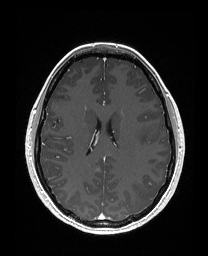
Brain MRI from a brain-tumour surgery series, one axial slice; slice 100 of 176 in the series (ordered by position); T1-weighted post-contrast; 1 mm slice thickness; 208 × 256 image matrix, field of view 203 × 250 mm. From the clinical record (not read from this slice): histopathology: Astrocytoma; WHO grade: 3; IDH mutation: yes.
Outlined on this slice (manually delineated by an expert):
- tumour: box from (x=132, y=126) to (x=154, y=145) px